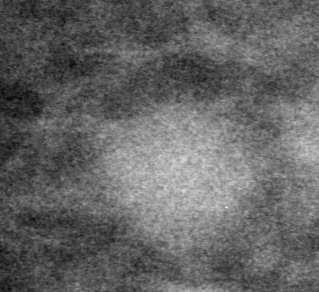
Region of interest cut from a scanned film mammogram (one marked finding); left breast; CC view; BI-RADS breast density category 1 (scale 1–4).
Mass, shape round, margins obscured; BI-RADS assessment category 0 (incomplete: needs additional imaging); pathology result (as recorded, not read from the image): benign.